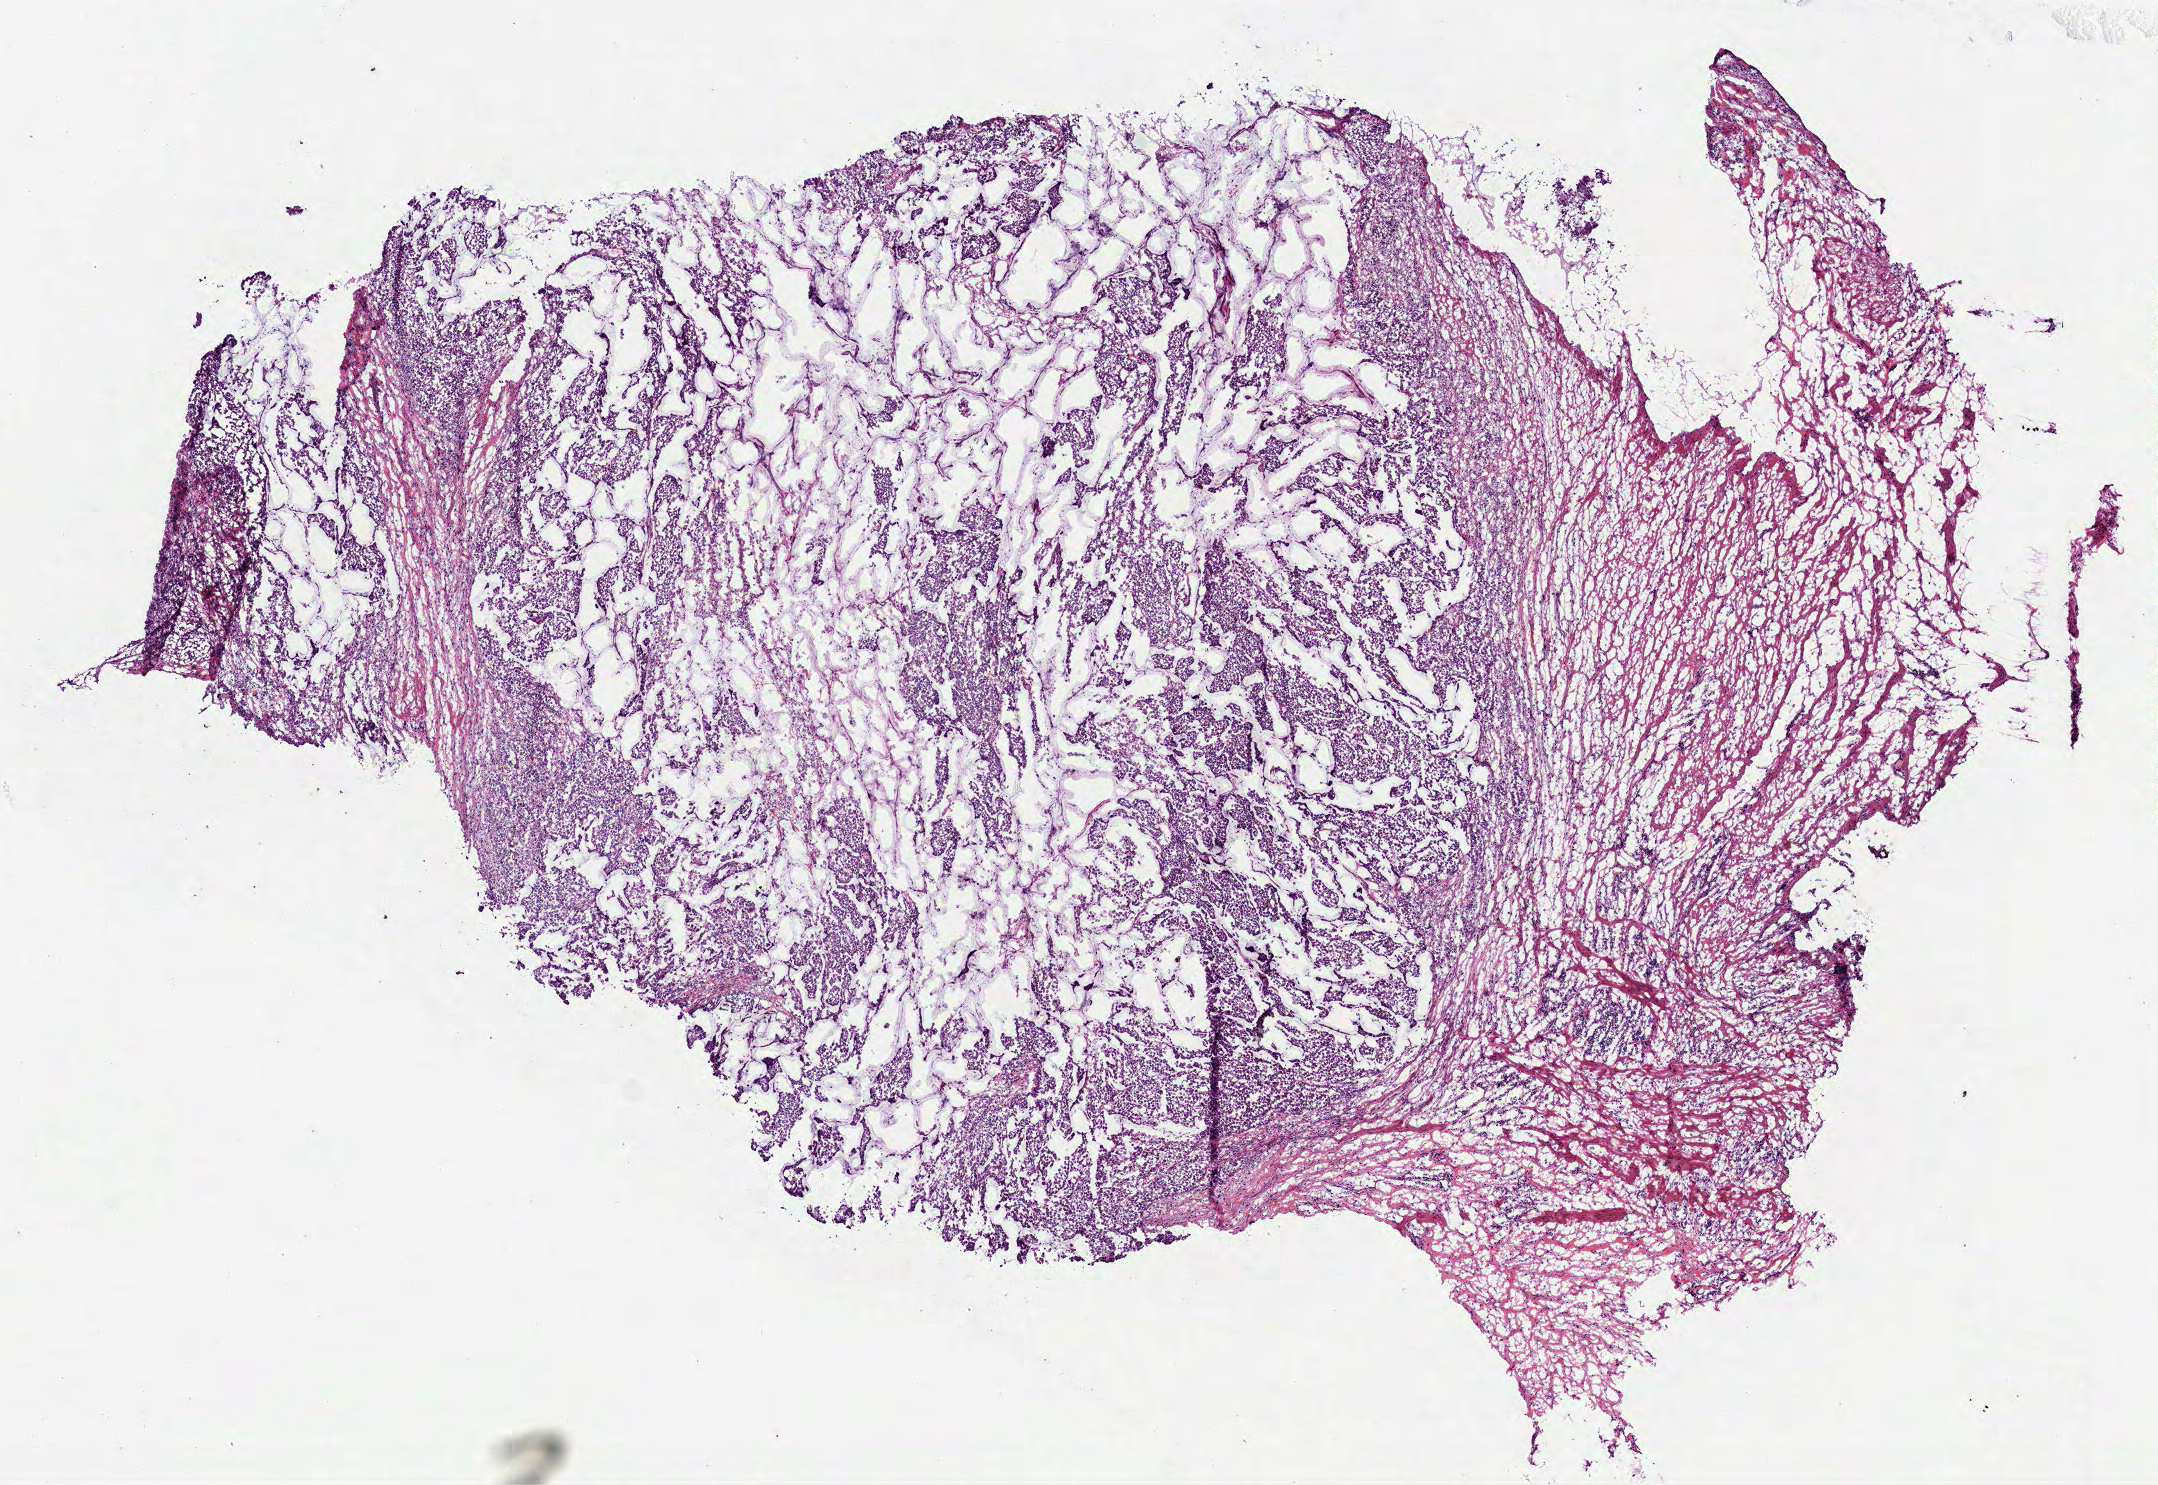
Digitized H&E tissue section (whole slide) — shown as a low-resolution overview of the whole scanned area (about 8.7 x 6.0 mm, acquisition: 40x scan), frozen section from the bottom of the tissue portion, primary tumour sample from the colon. Patient: female, age at initial diagnosis 71 years. Composition of this section per pathologist review: tumour cells 80%, tumour nuclei 80%, normal cells 0%, stromal cells 20%, necrosis 0%.
• diagnosis: Adenocarcinoma, NOS (ascending colon)
• AJCC pathologic stage: I (6th edition)